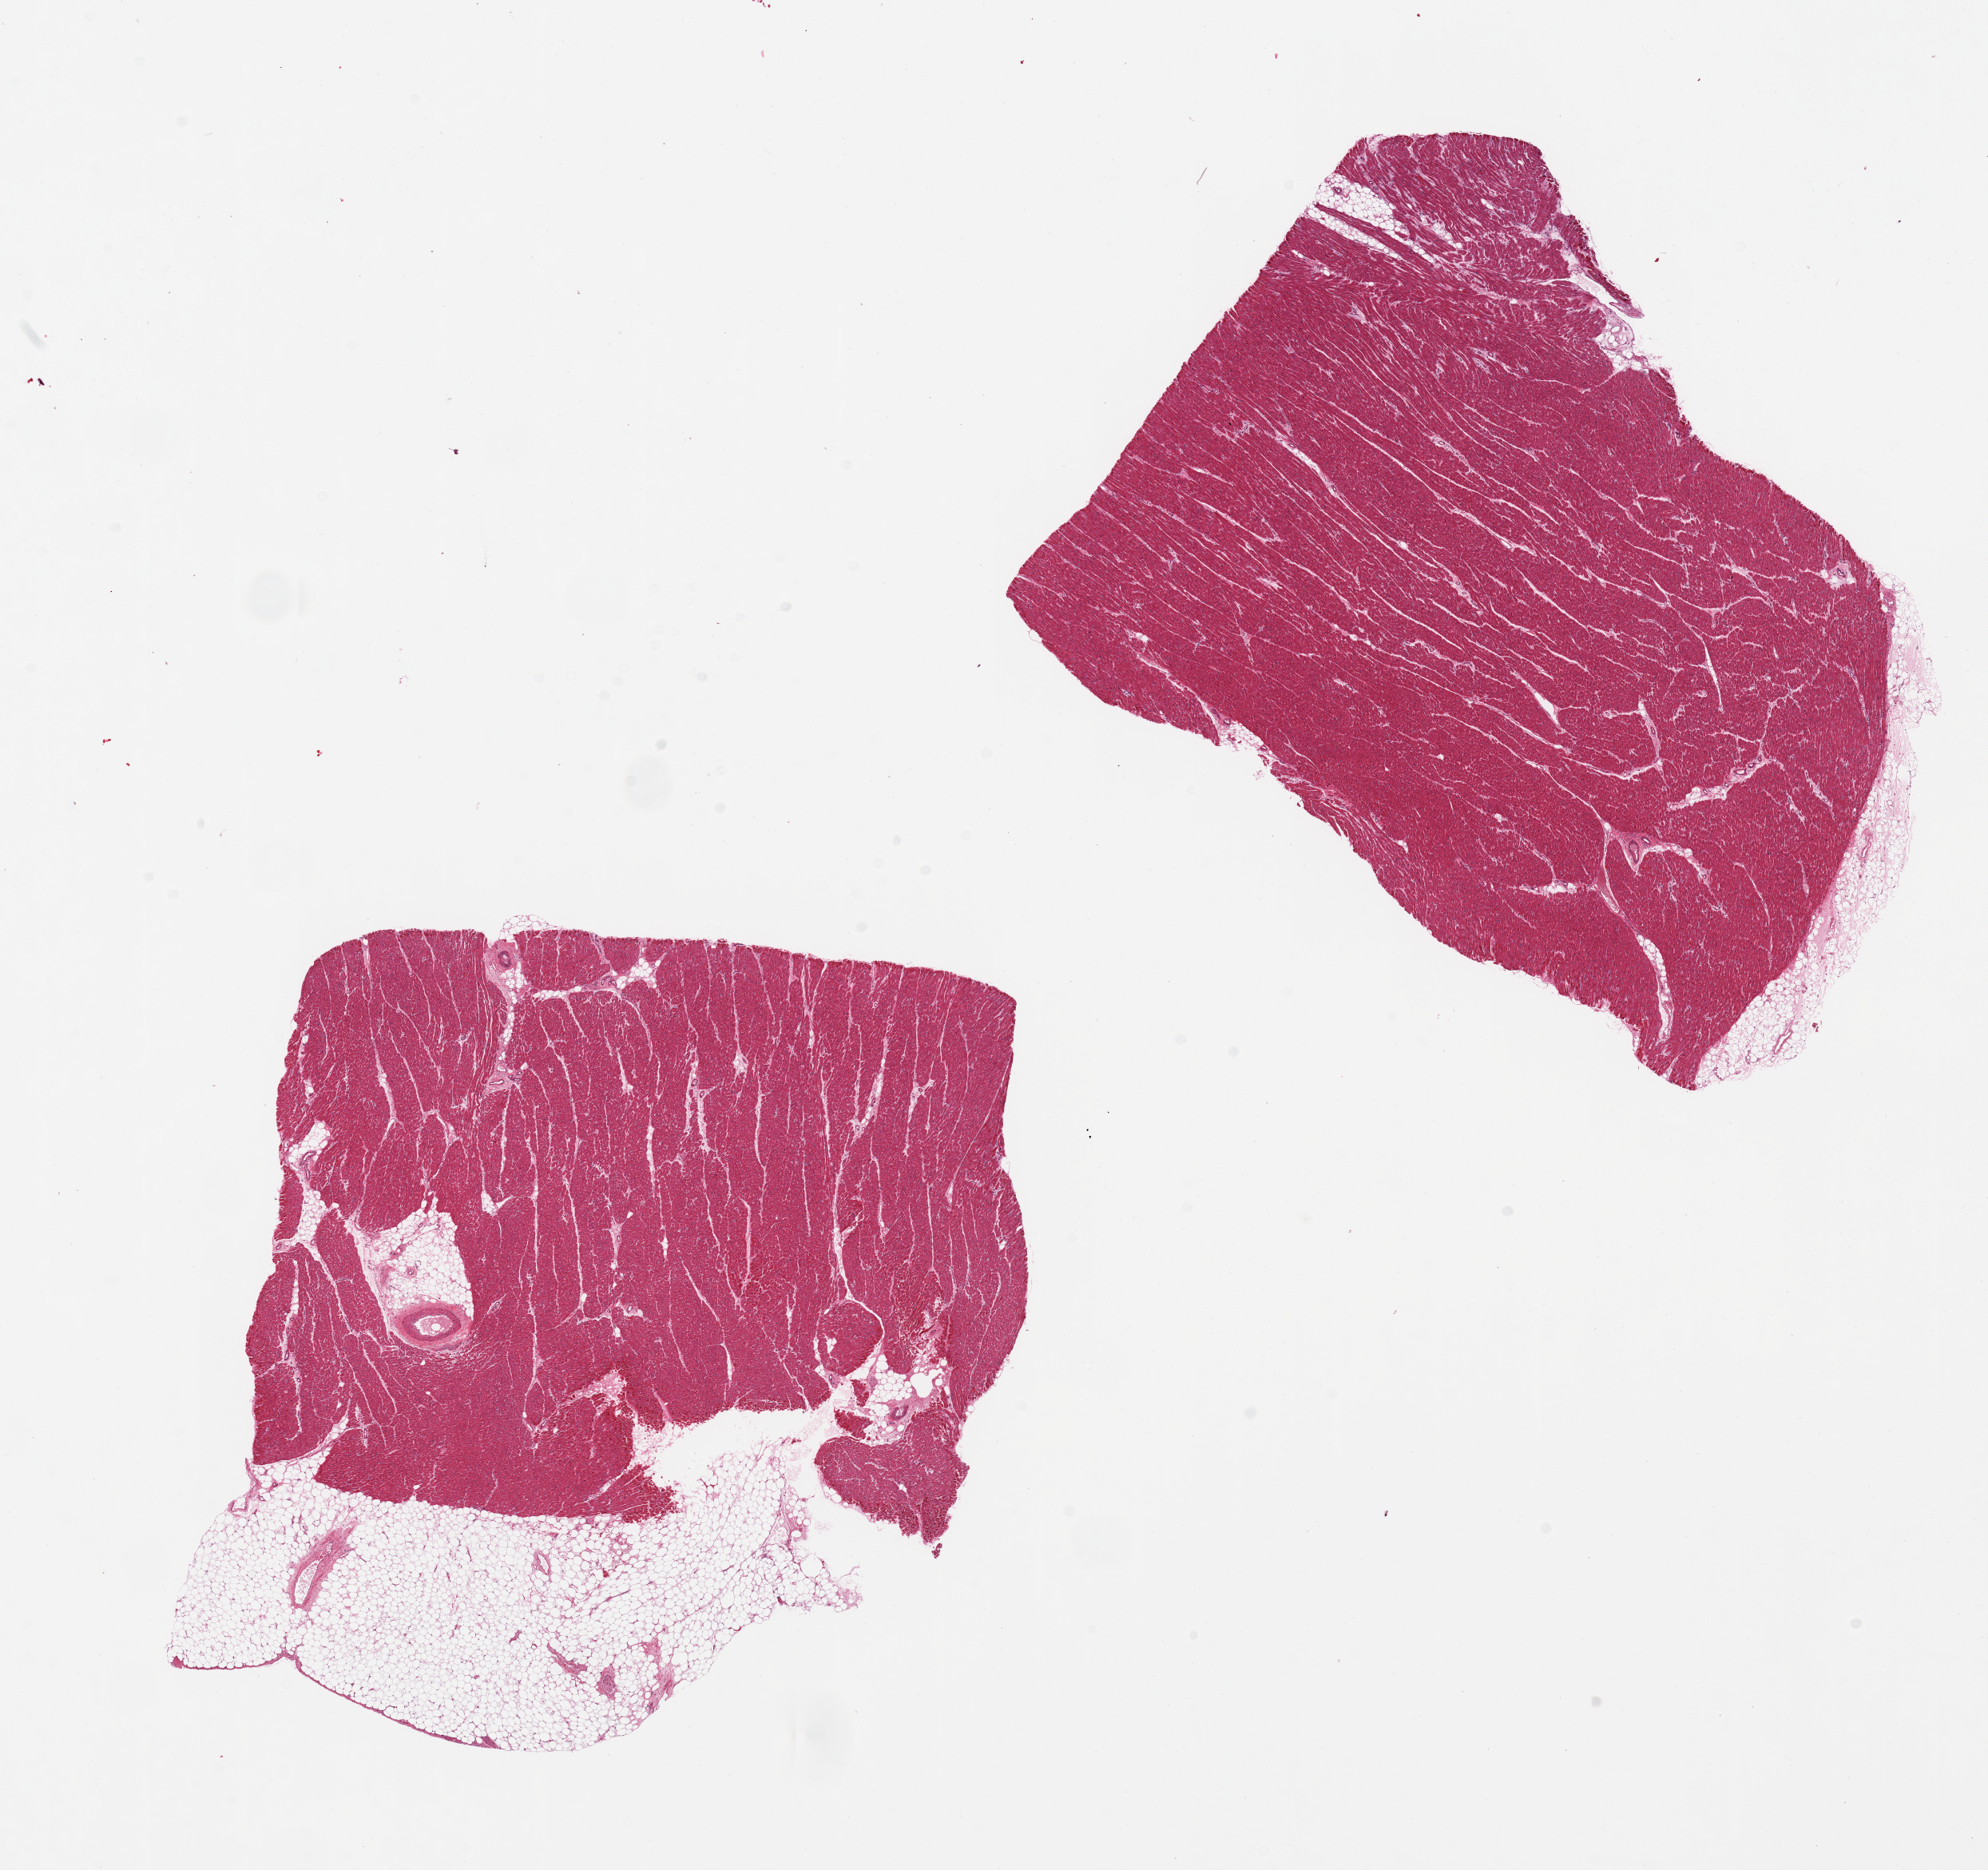
Whole-slide image, haematoxylin and eosin stain, shown as a low-resolution overview of the whole scanned area (about 19.7 x 18.5 mm), PAXgene-fixed paraffin-embedded (PFPE) section, section of heart (target tissue), tissue donor sample. Donor sex: female.
• reviewer comment on this tissue sample: 2 pieces, both with attached adipose tissue (5-10% on one, 25% on second)